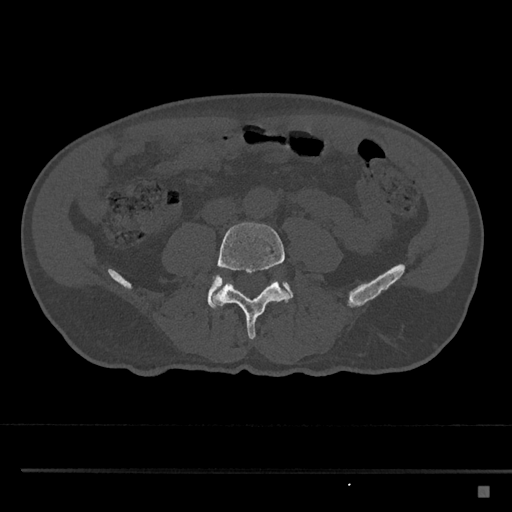
CT including the spine, one axial slice. Position 627 of 797 along the scan axis. Reconstruction kernel Br40s/3. 120 kVp. Bone window (W 1800 / L 400 HU). 0.5 mm slice thickness. 512 × 512 image matrix. Male patient, age 59 years. Case-level facts recorded for this patient, not image findings: primary cancer: prostate.
Annotated regions visible in this slice (semi-automatic segmentation, software-assisted and operator-edited):
- L4 vertebra: bounding box <212,222,290,339> (left, top, right, bottom; pixels)
- L5 vertebra: <207,275,294,309>